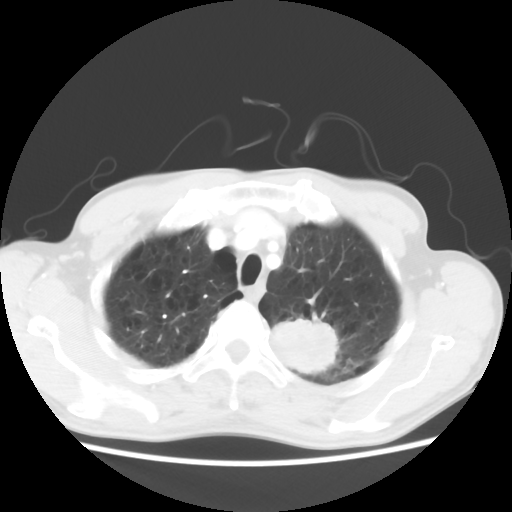
Chest CT, one axial slice; slice 53 of 64 in the series (ordered by position); reconstruction kernel STANDARD; 120 kVp; lung window (W 1500 / L -600 HU); 5 mm slice thickness; 512 × 512 image matrix. Male patient, age 63 years. Case-level facts recorded for this patient, not image findings: clinical TNM (as recorded): T2 N0 M0.
Annotated regions visible in this slice (rectangle marked by the reading radiologist):
- lung tumour (recorded histology: adenocarcinoma): bounding box [x1, y1, x2, y2] px = [269, 311, 345, 386]